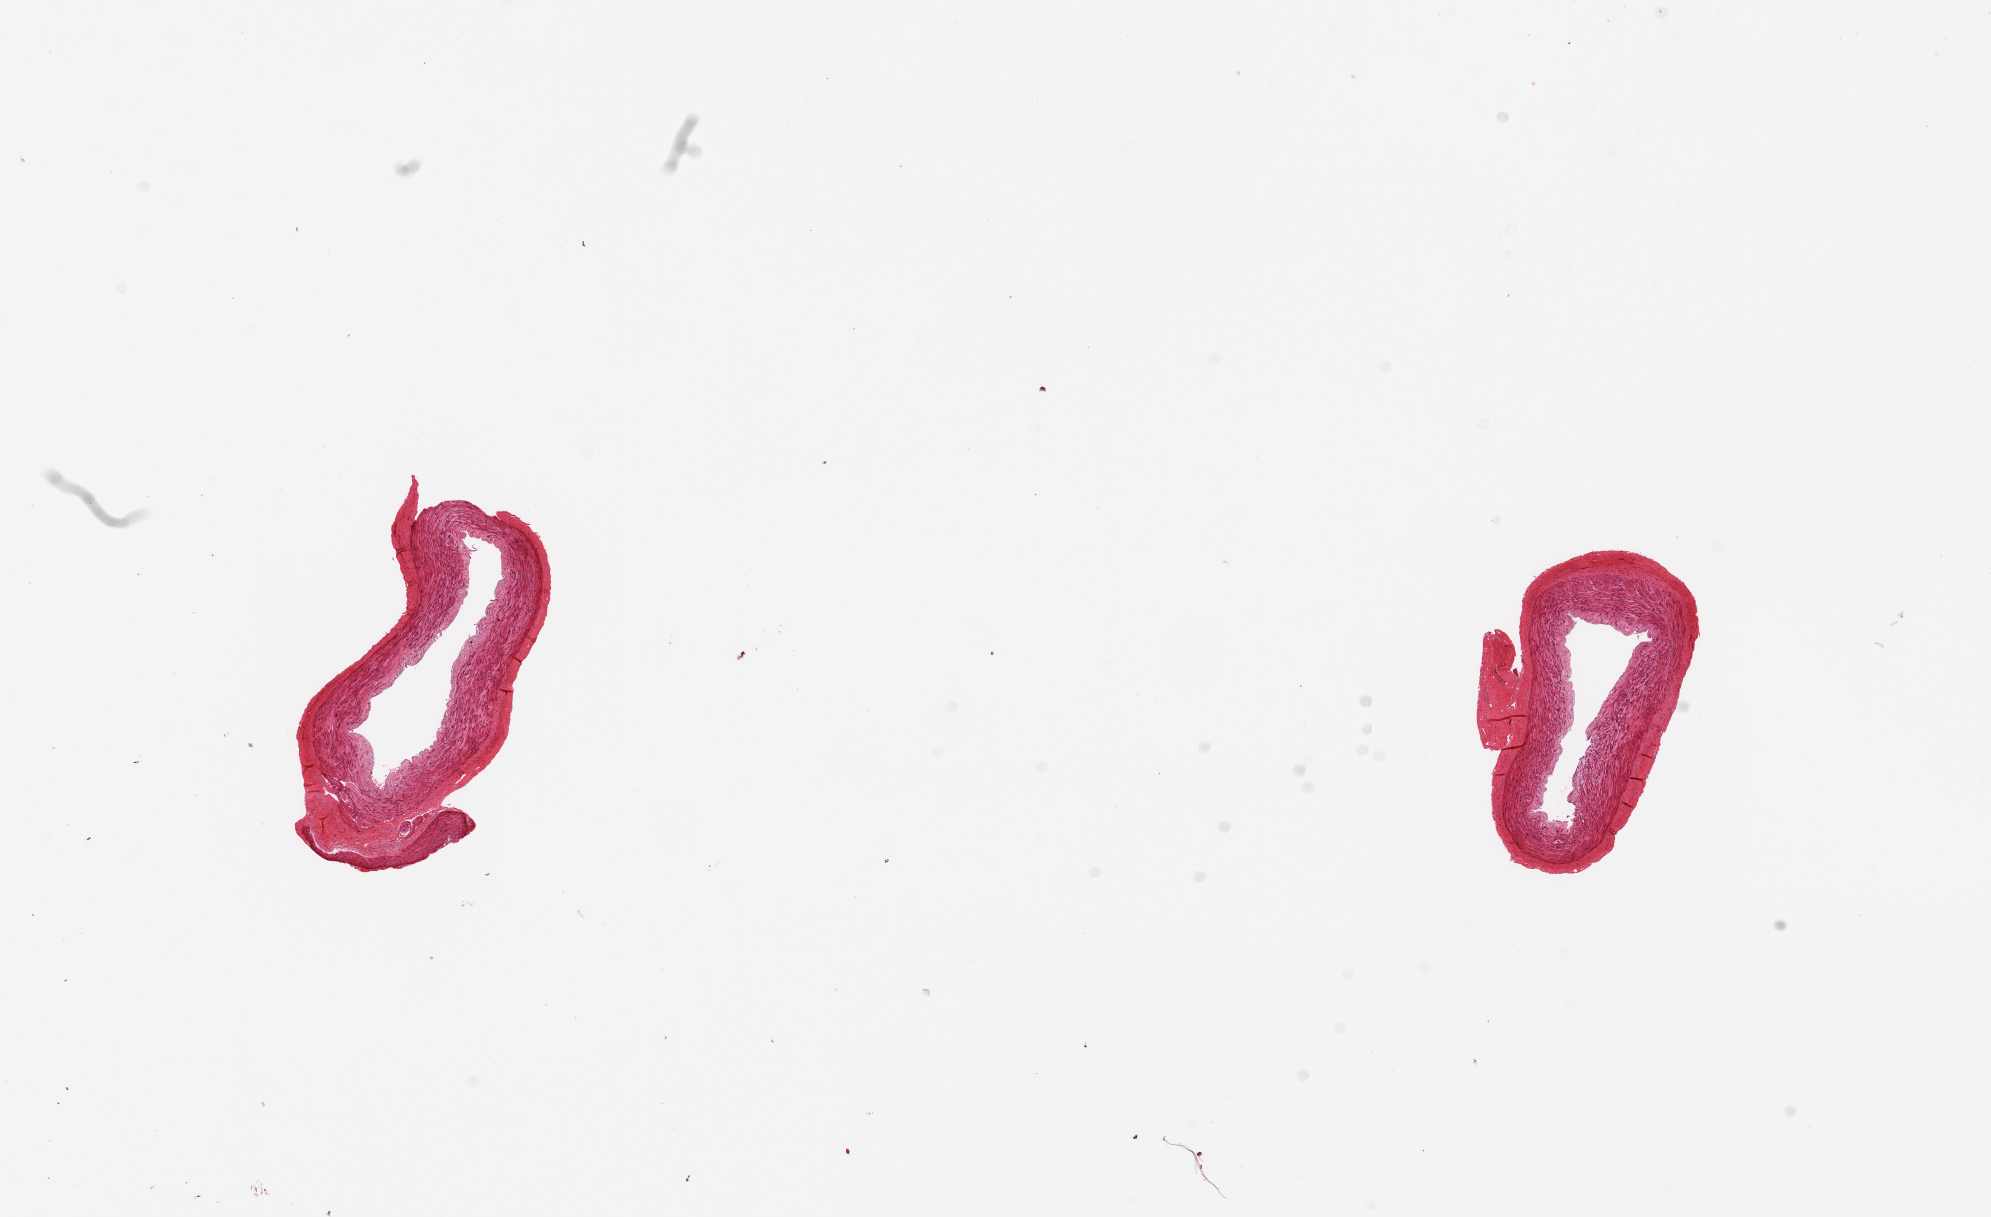
Whole-slide image, haematoxylin and eosin stain, brightfield, low-resolution overview of the scanned area, about 15.8 x 9.6 mm. PAXgene-fixed, paraffin-embedded tissue. Section of tibial artery (target tissue). Tissue donor sample. Donor sex: female.
Pathologist's review note for this sample: 2 pieces; no lesions, well trimmed.